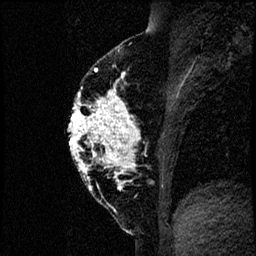
Breast MRI (dynamic contrast-enhanced), one sagittal slice; slice 37 of 60 in the series (ordered by position); dynamic contrast-enhanced study with each time point stored as its own series, time point 2 of 4 at this slice position (early post-contrast, ordered by acquisition time); 1.5 T; TE 4.2 ms, TR 17.6 ms; 2 mm slice thickness; 256 × 256 image matrix, field of view 200 × 200 mm. Patient: female, 40 years. From the clinical record (not read from this slice): setting: breast cancer imaged before/during neoadjuvant chemotherapy; receptor status: HER2-positive.
Structures marked on this image (semi-automatic segmentation, software-assisted and operator-edited):
- analysis volume of interest (the breast-tissue region the enhancement analysis was run in; not a lesion): bounding box (x1, y1, x2, y2) in pixels: (66, 55, 185, 206)
- tumour enhancement mask (voxels above the 100 % enhancement threshold inside the analysis volume of interest): (68, 69, 137, 179)